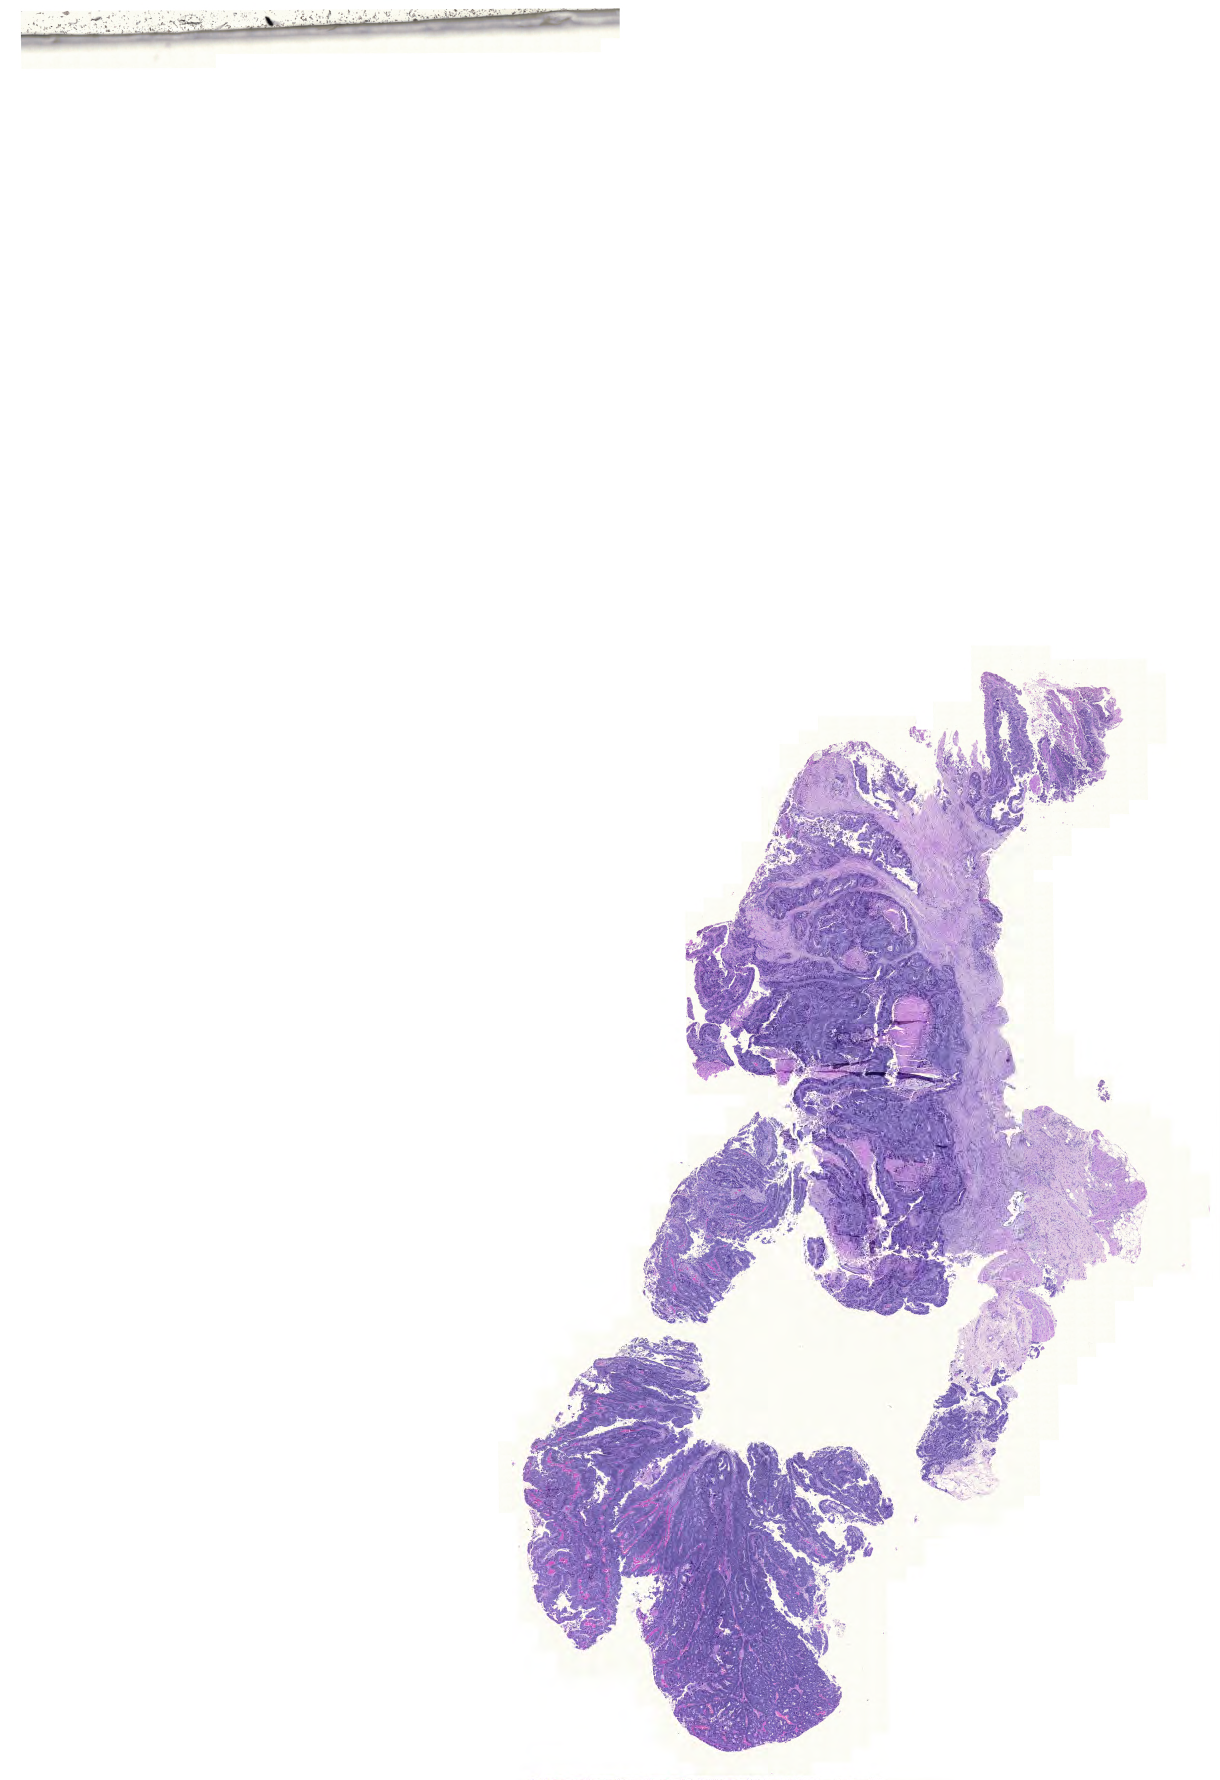
Whole-slide histology image, Hematoxylin and eosin (H&E) stained — a low-resolution overview of the entire scanned area, about 18.2 x 26.5 mm (from a 20x scan), formalin-fixed paraffin-embedded (FFPE) diagnostic section, sample: primary tumour, colon. Male patient; age at initial diagnosis 72 years.
Histologic diagnosis: Adenocarcinoma, NOS.